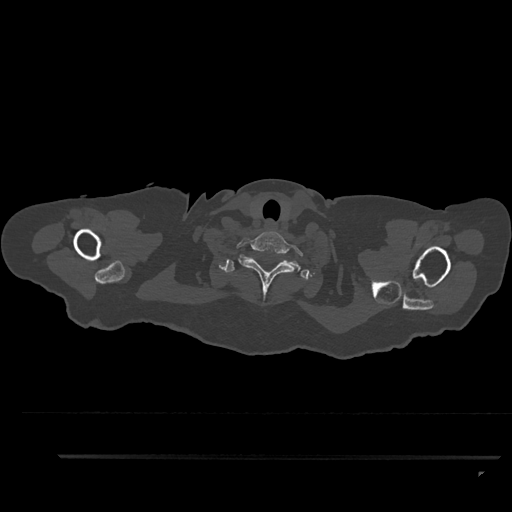
CT including the spine, one axial slice; position 785 of 797 along the scan axis; reconstruction kernel Br40s/3; 120 kVp; bone window (W 1800 / L 400 HU); 0.5 mm slice thickness; 512 × 512 image matrix, field of view 408 × 408 mm. Female patient, age 44 years. Case-level facts recorded for this patient, not image findings: primary cancer: renal; vertebrae with lytic lesions (as recorded): L1.
Structures marked on this image (semi-automatically segmented with operator editing):
- T1 vertebra: box from (x=219, y=255) to (x=309, y=280) px